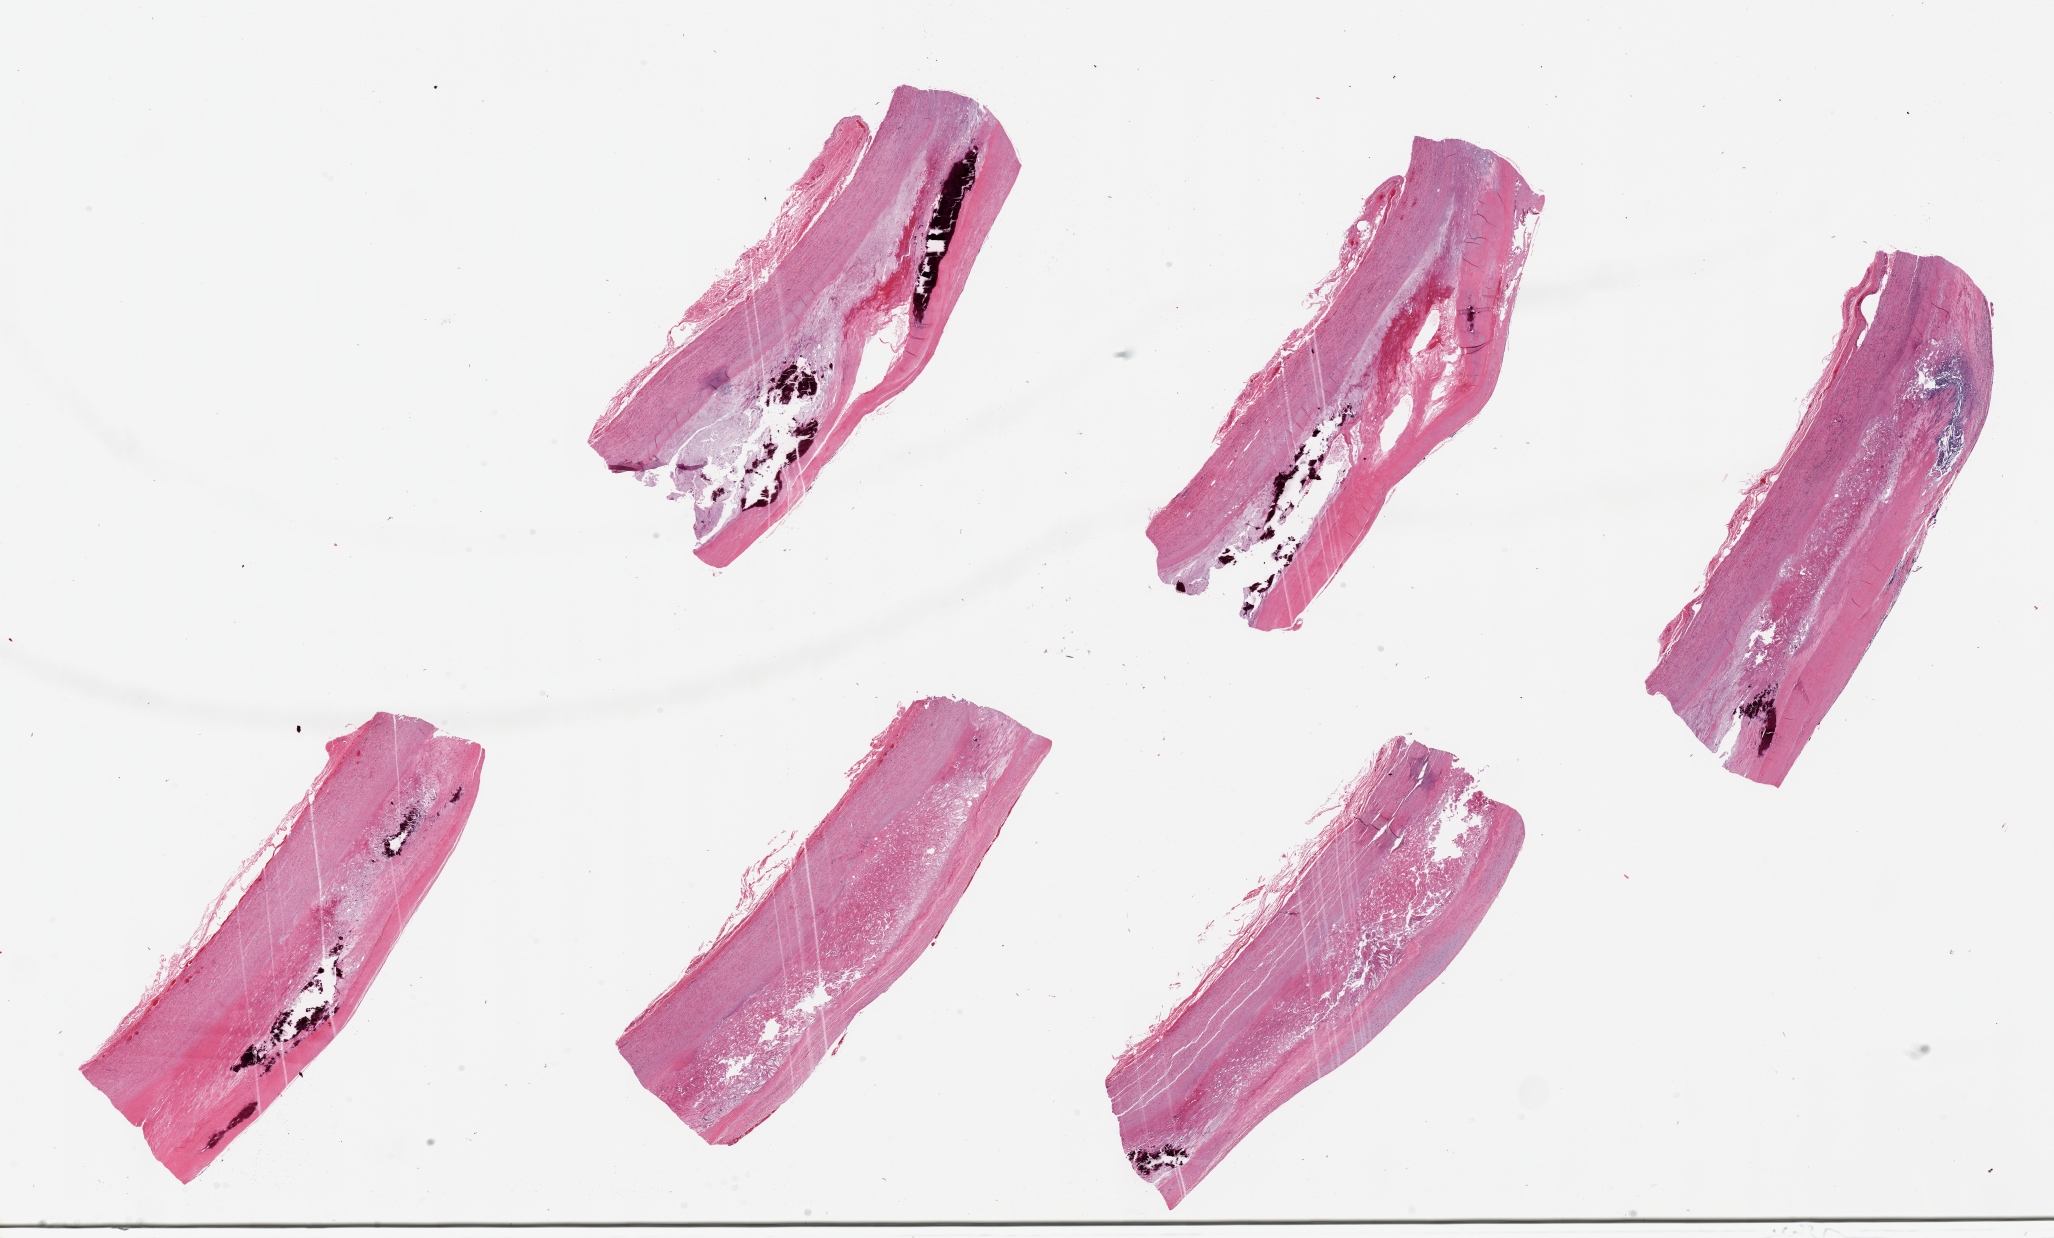
Haematoxylin and eosin whole-slide image, whole scanned area (about 32.5 x 19.6 mm) shown as a low-resolution overview; PAXgene-fixed, paraffin-embedded tissue; section of aorta (target tissue); tissue donor sample.
• review note (as recorded): 6 pieces, up to 8x3mm; all with extensive atheromatous, calcified, hemorrhagic plaques; little uninvolved tissue remains